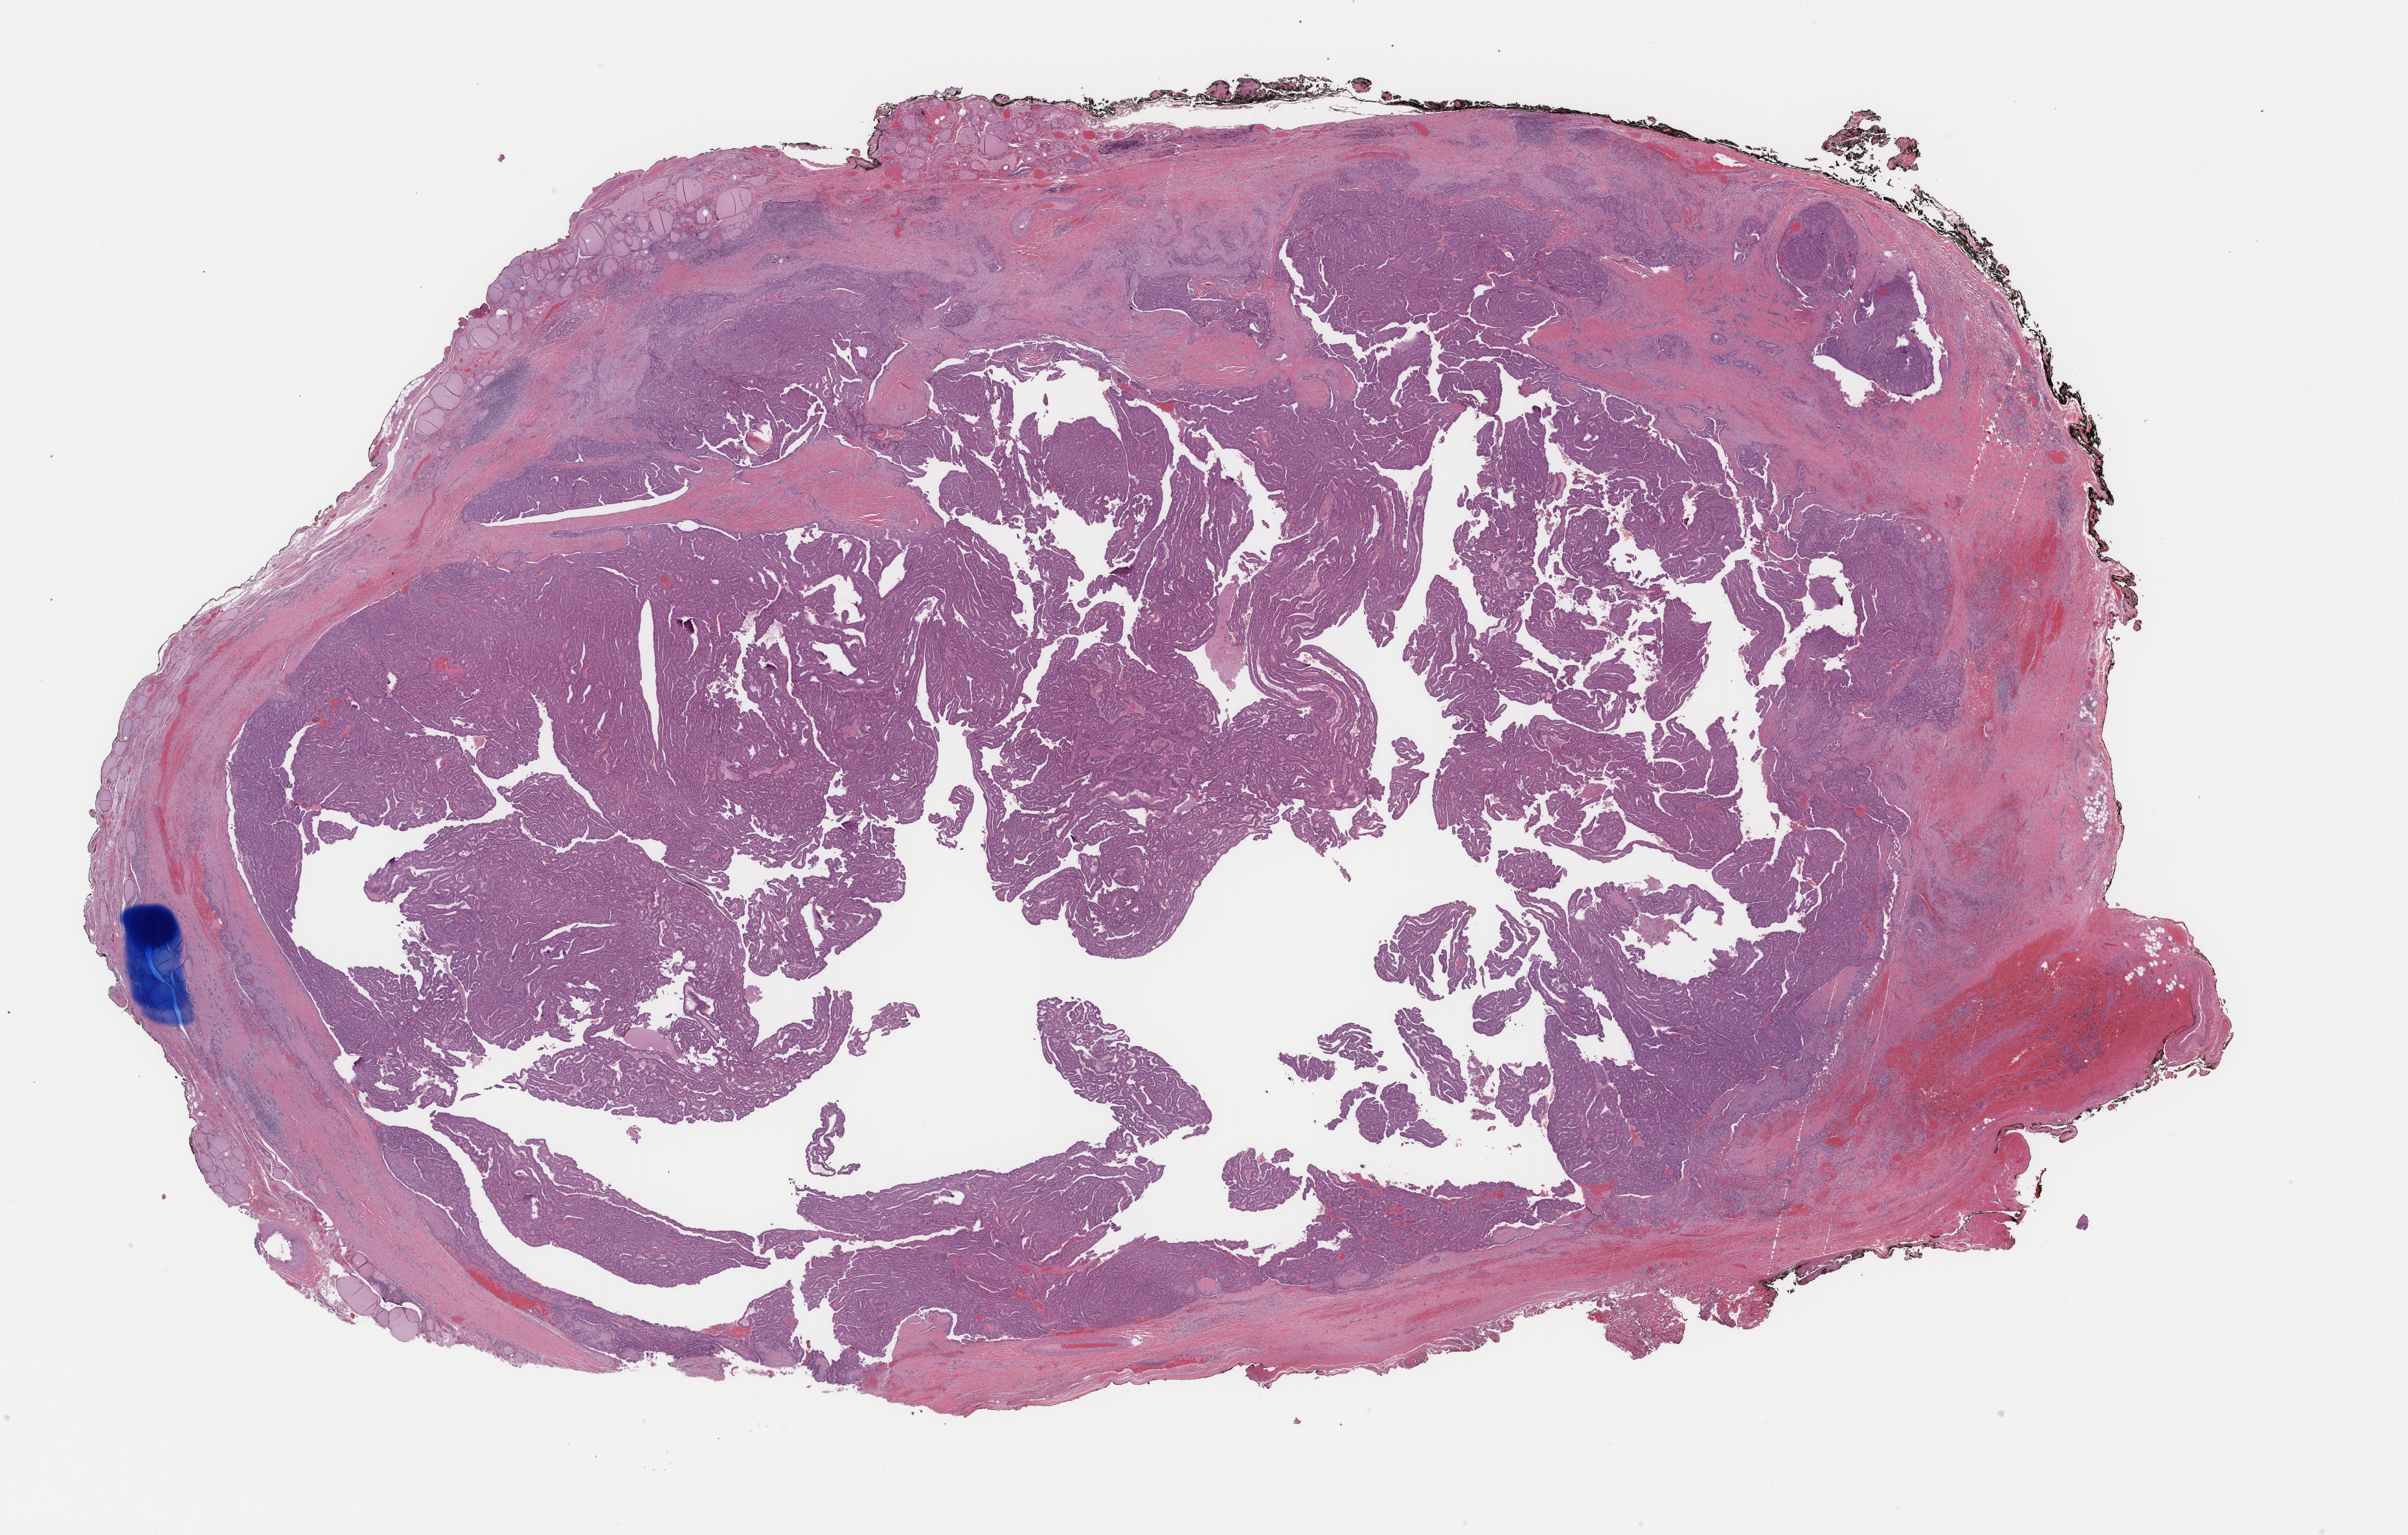
Digitized H&E-stained tissue section (whole slide) — whole scanned area (about 29.5 x 18.8 mm, slide scanned at 40x) shown as a low-resolution overview. Formalin-fixed paraffin-embedded (FFPE) diagnostic section. Sample: primary tumour, thyroid. Female patient; age at initial diagnosis 41 years.
* TNM: T2 N1 M0
* histologic diagnosis: Papillary adenocarcinoma, NOS (thyroid gland)
* AJCC pathologic stage: I
* lymph nodes positive (case pathology): 2 of 7 examined